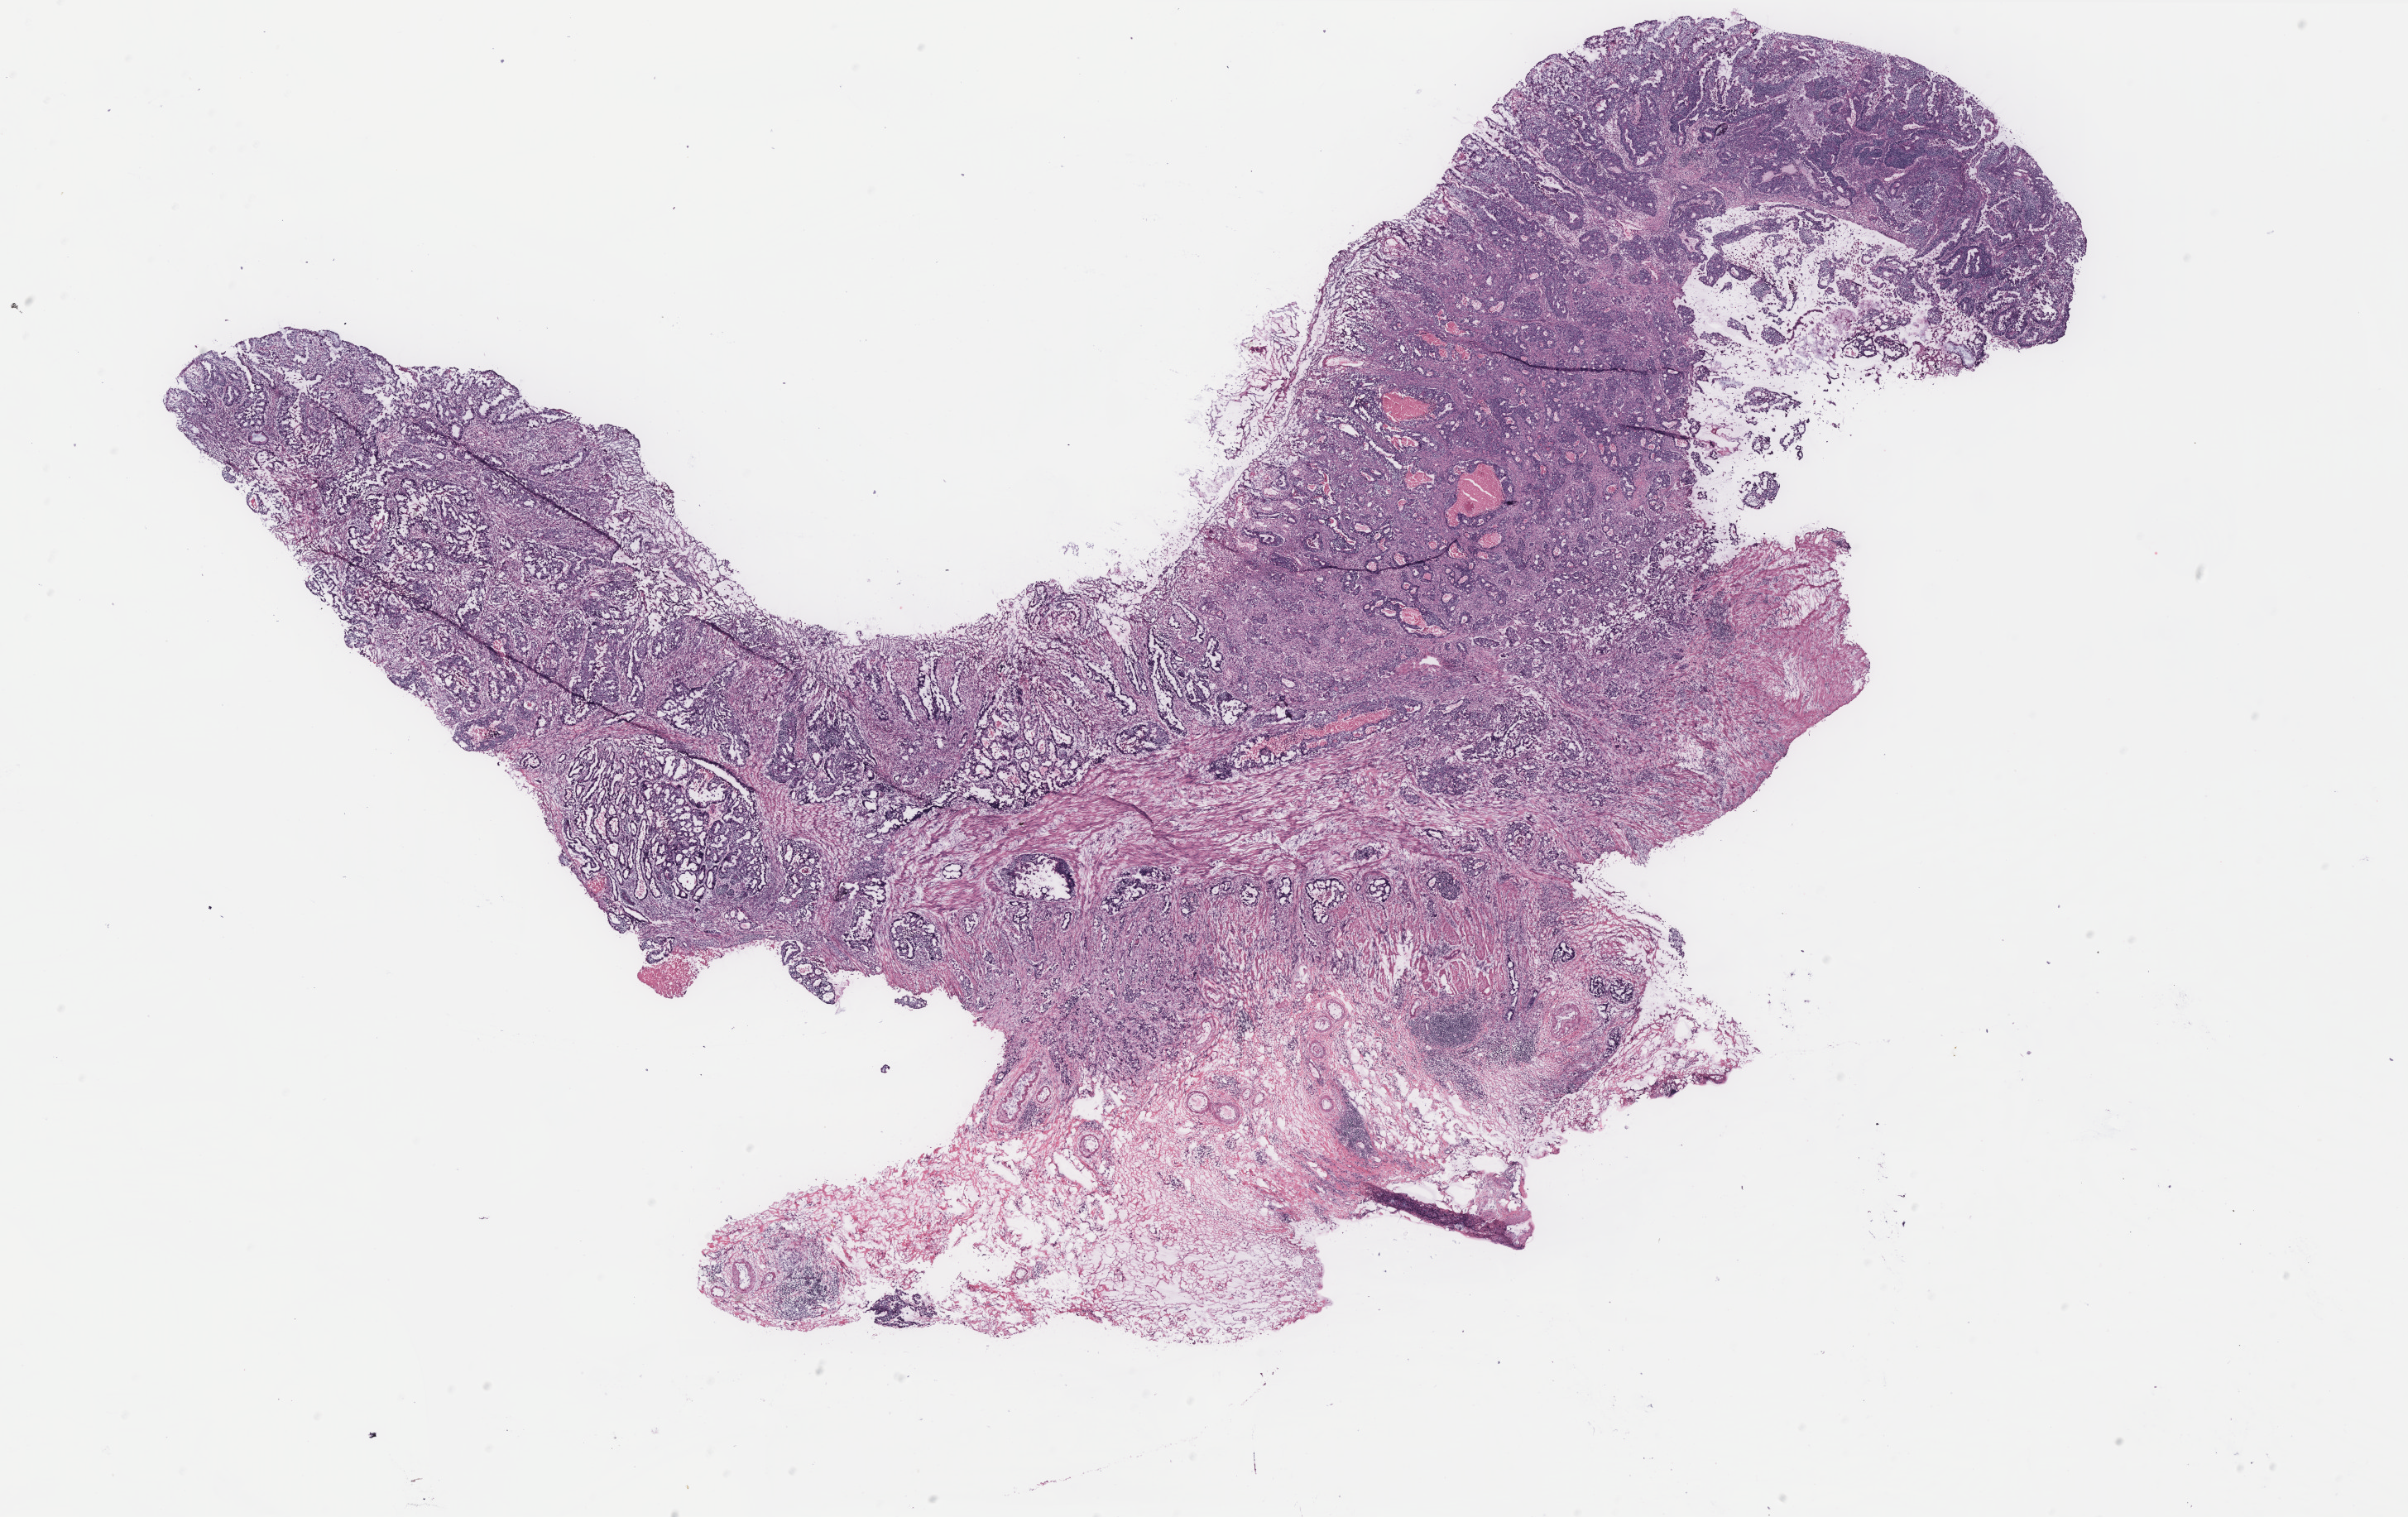
H&E whole-slide image — whole scanned area (about 23.3 x 14.7 mm, from a 40x scan) shown as a low-resolution overview. Colon, tissue type not recorded.
Patient diagnosis (cohort enrolment): colon cancer (colon).